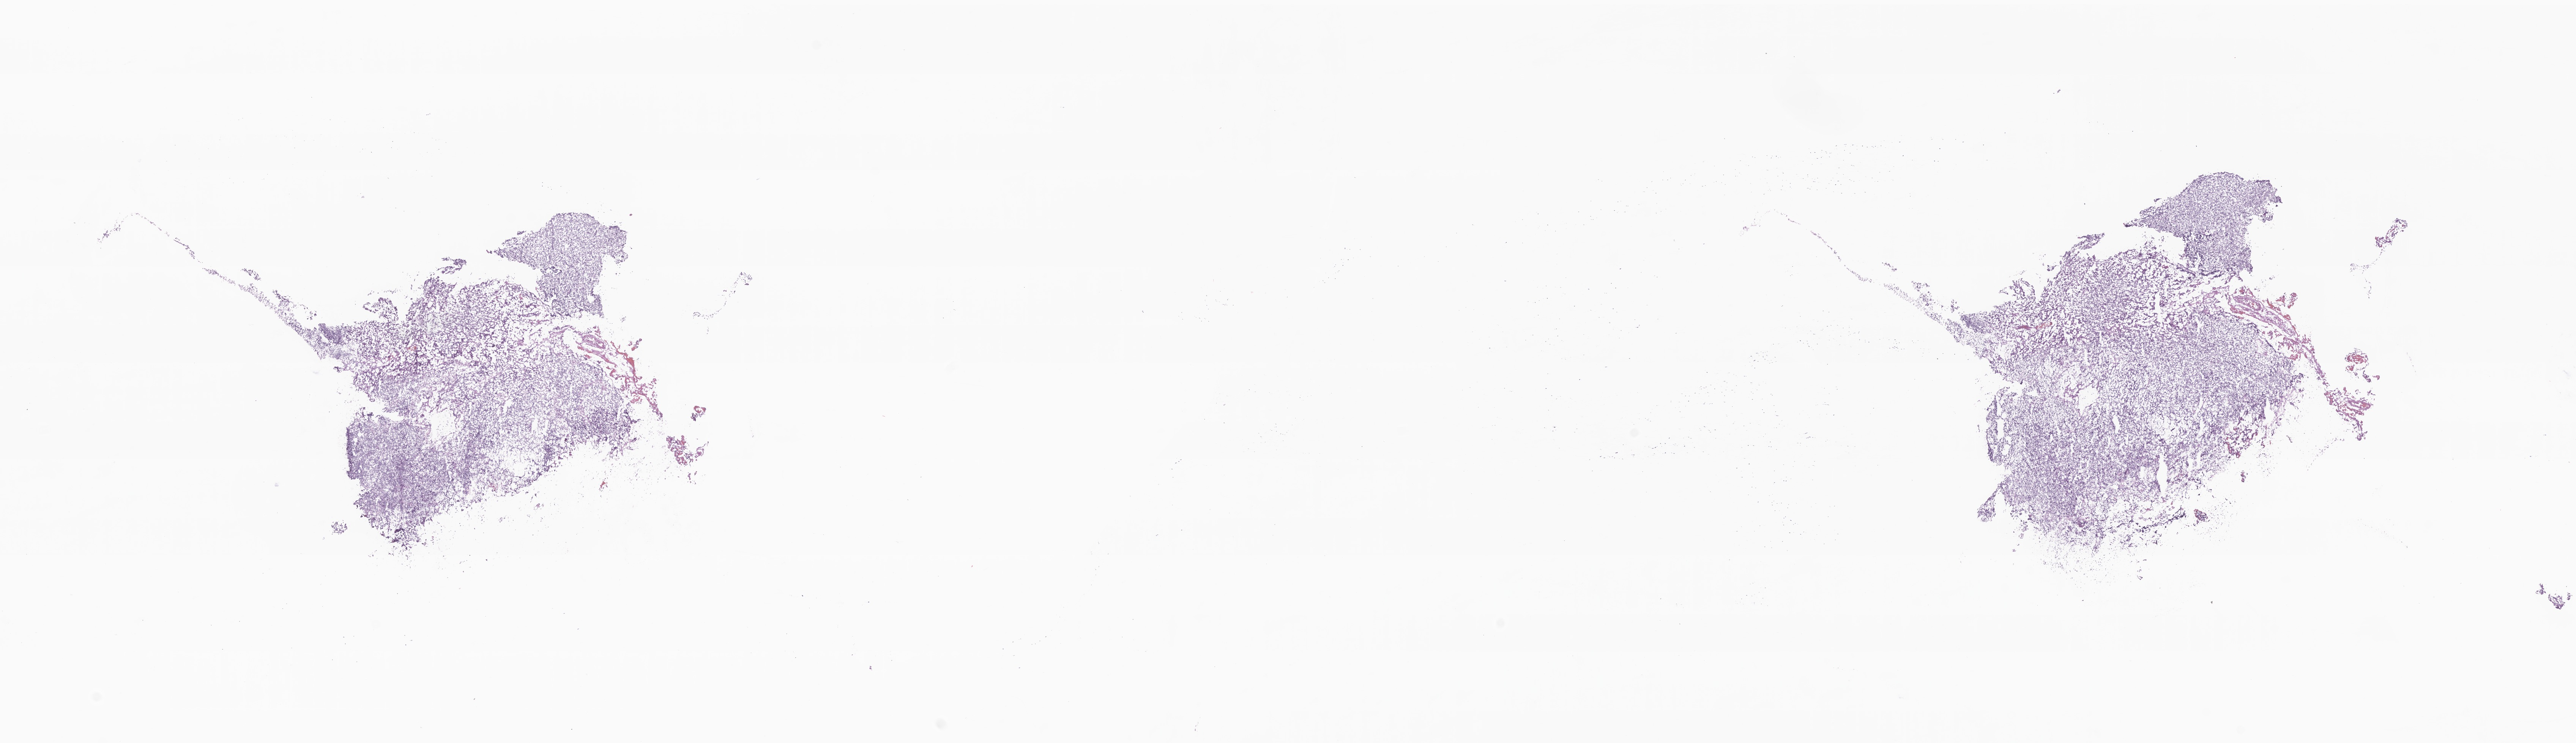
Whole-slide image, hematoxylin and eosin (H&E) stain of tumor tissue from the brain — a low-resolution overview of the entire scanned area, about 28.6 x 8.2 mm, frozen section (OCT-embedded). Patient: female, age 38 months (3 years 2 months).
Diagnosis (ICD-O-3 morphology term): Medulloblastoma, NOS.